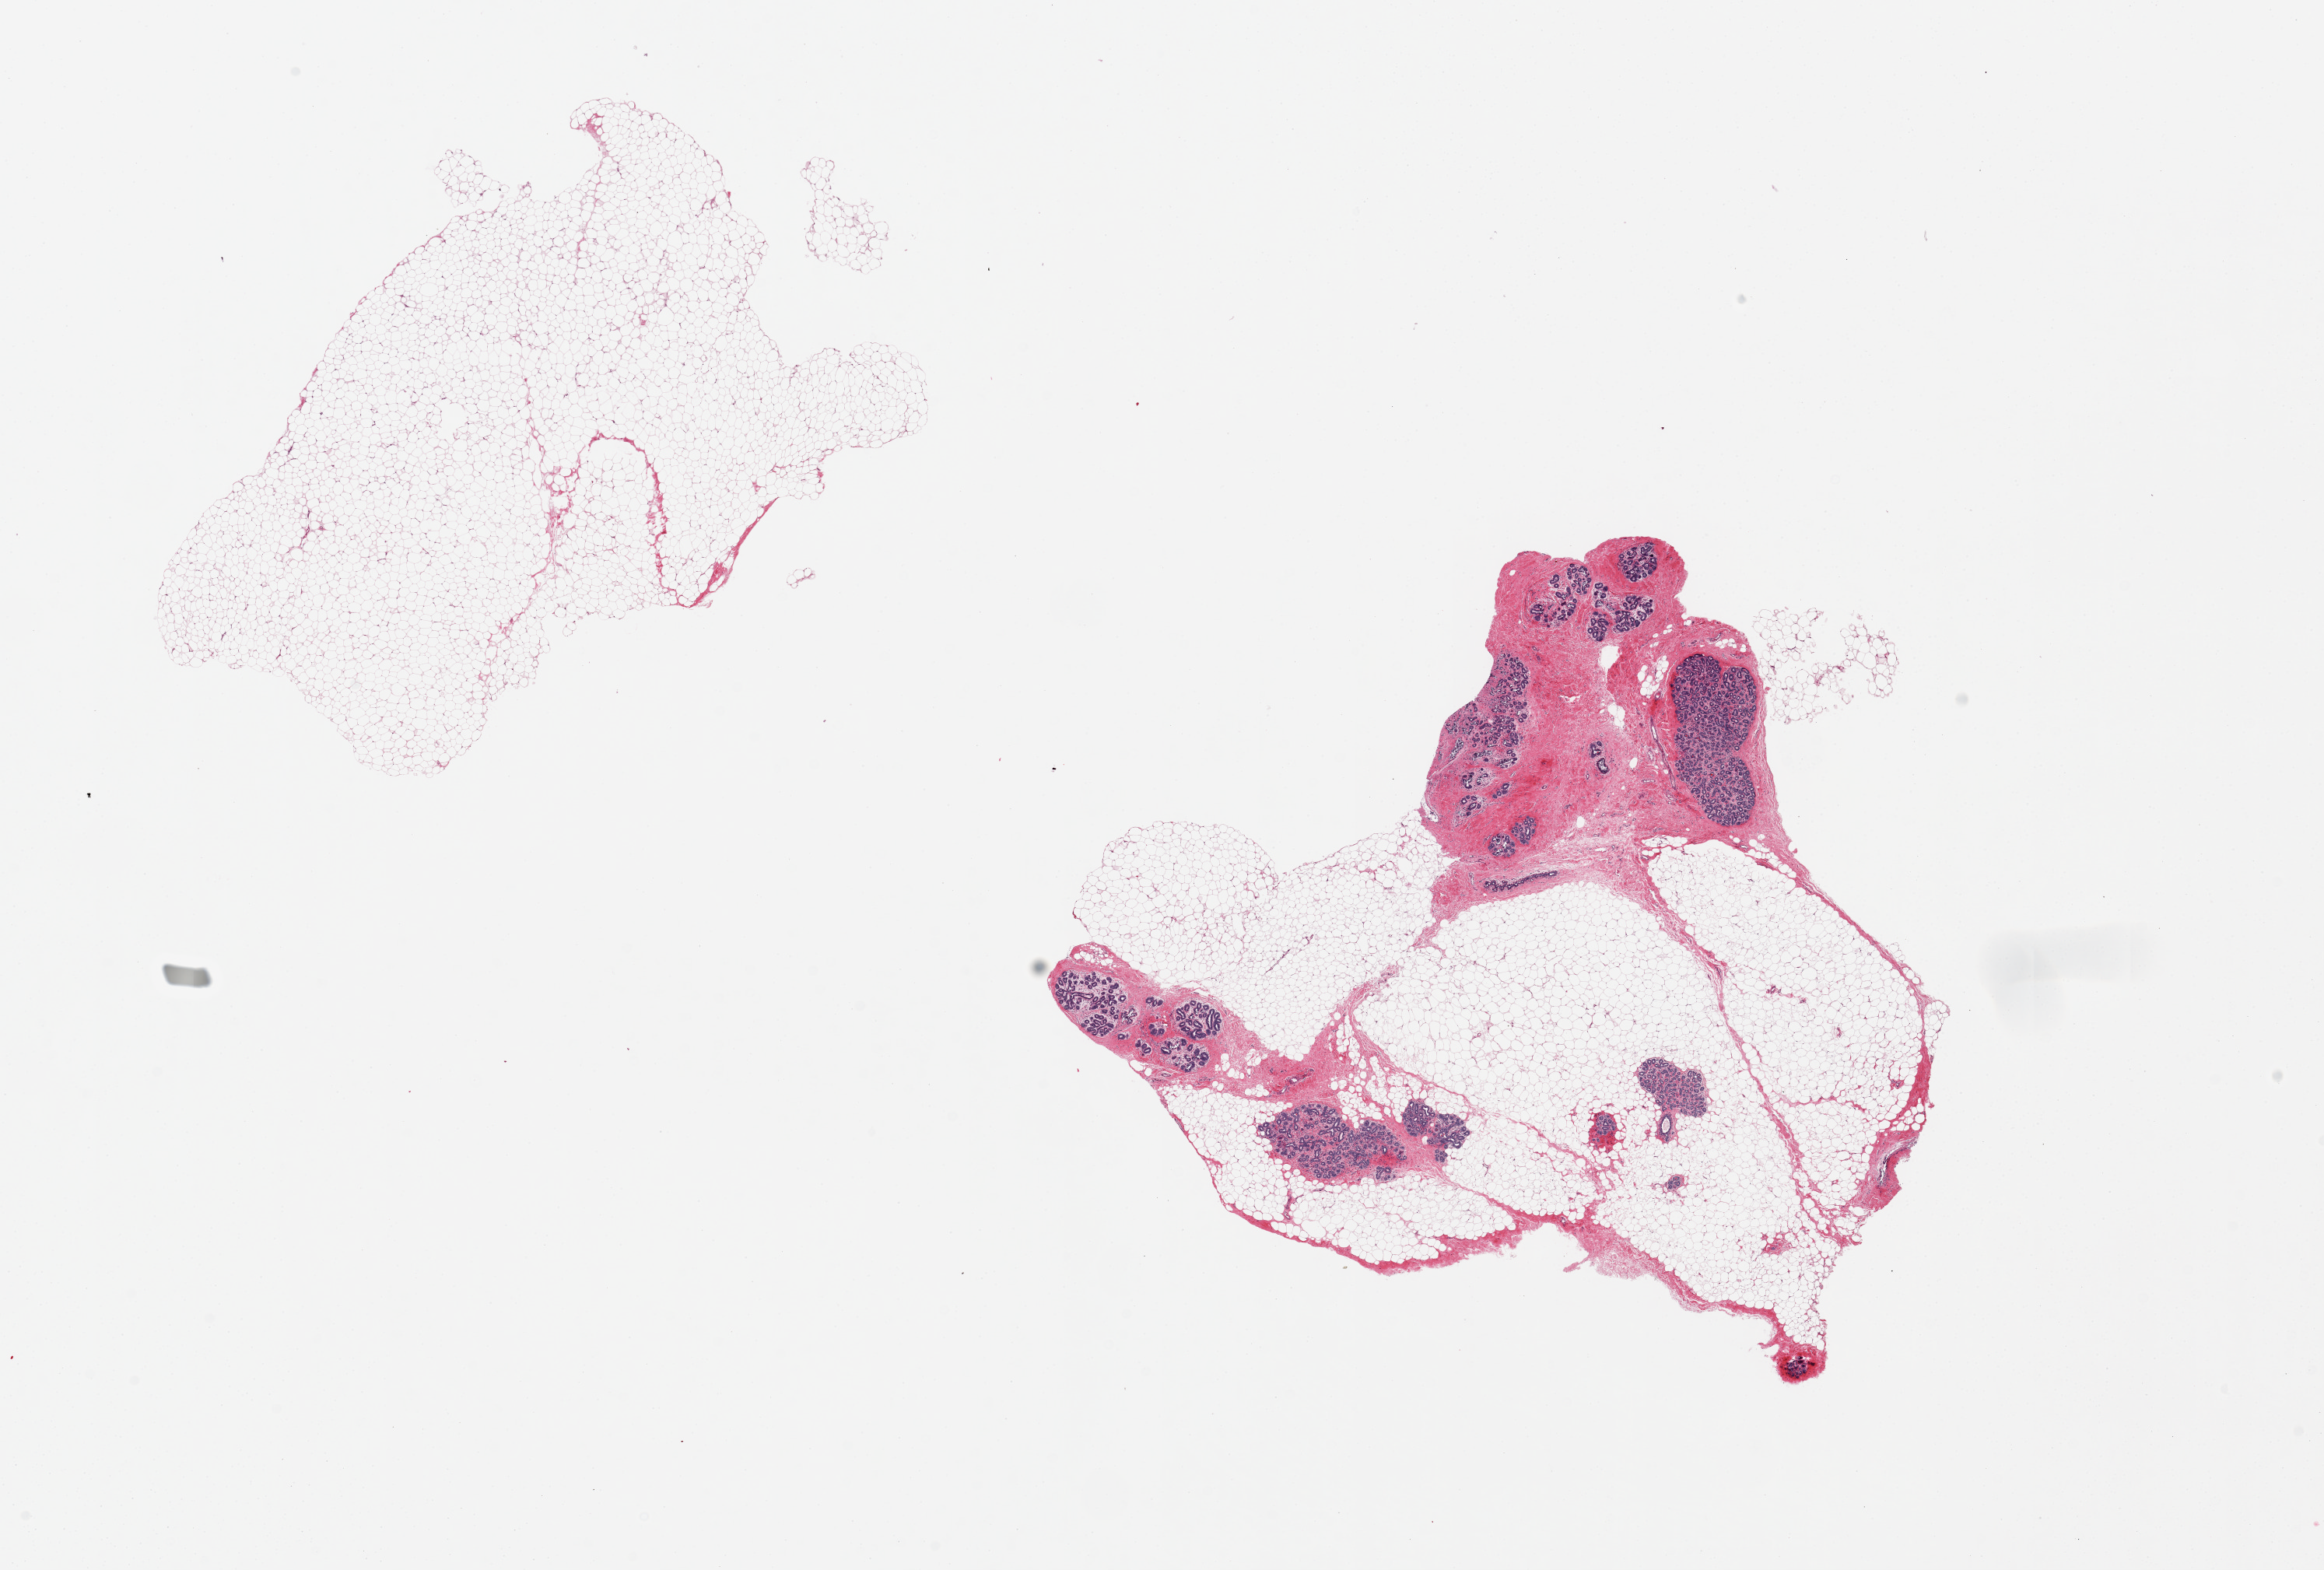
Digitized haematoxylin and eosin-stained section, brightfield — shown as a low-resolution overview of the whole scanned area (about 23.6 x 16.0 mm, from a 20x scan), PAXgene-fixed paraffin-embedded (PFPE) section, target tissue: breast, donor tissue sample. Donor sex: female.
Review note (as recorded): 2 pieces, one all fat, the other with areas of prominent adenosis/fibrocystic change, dominant area.